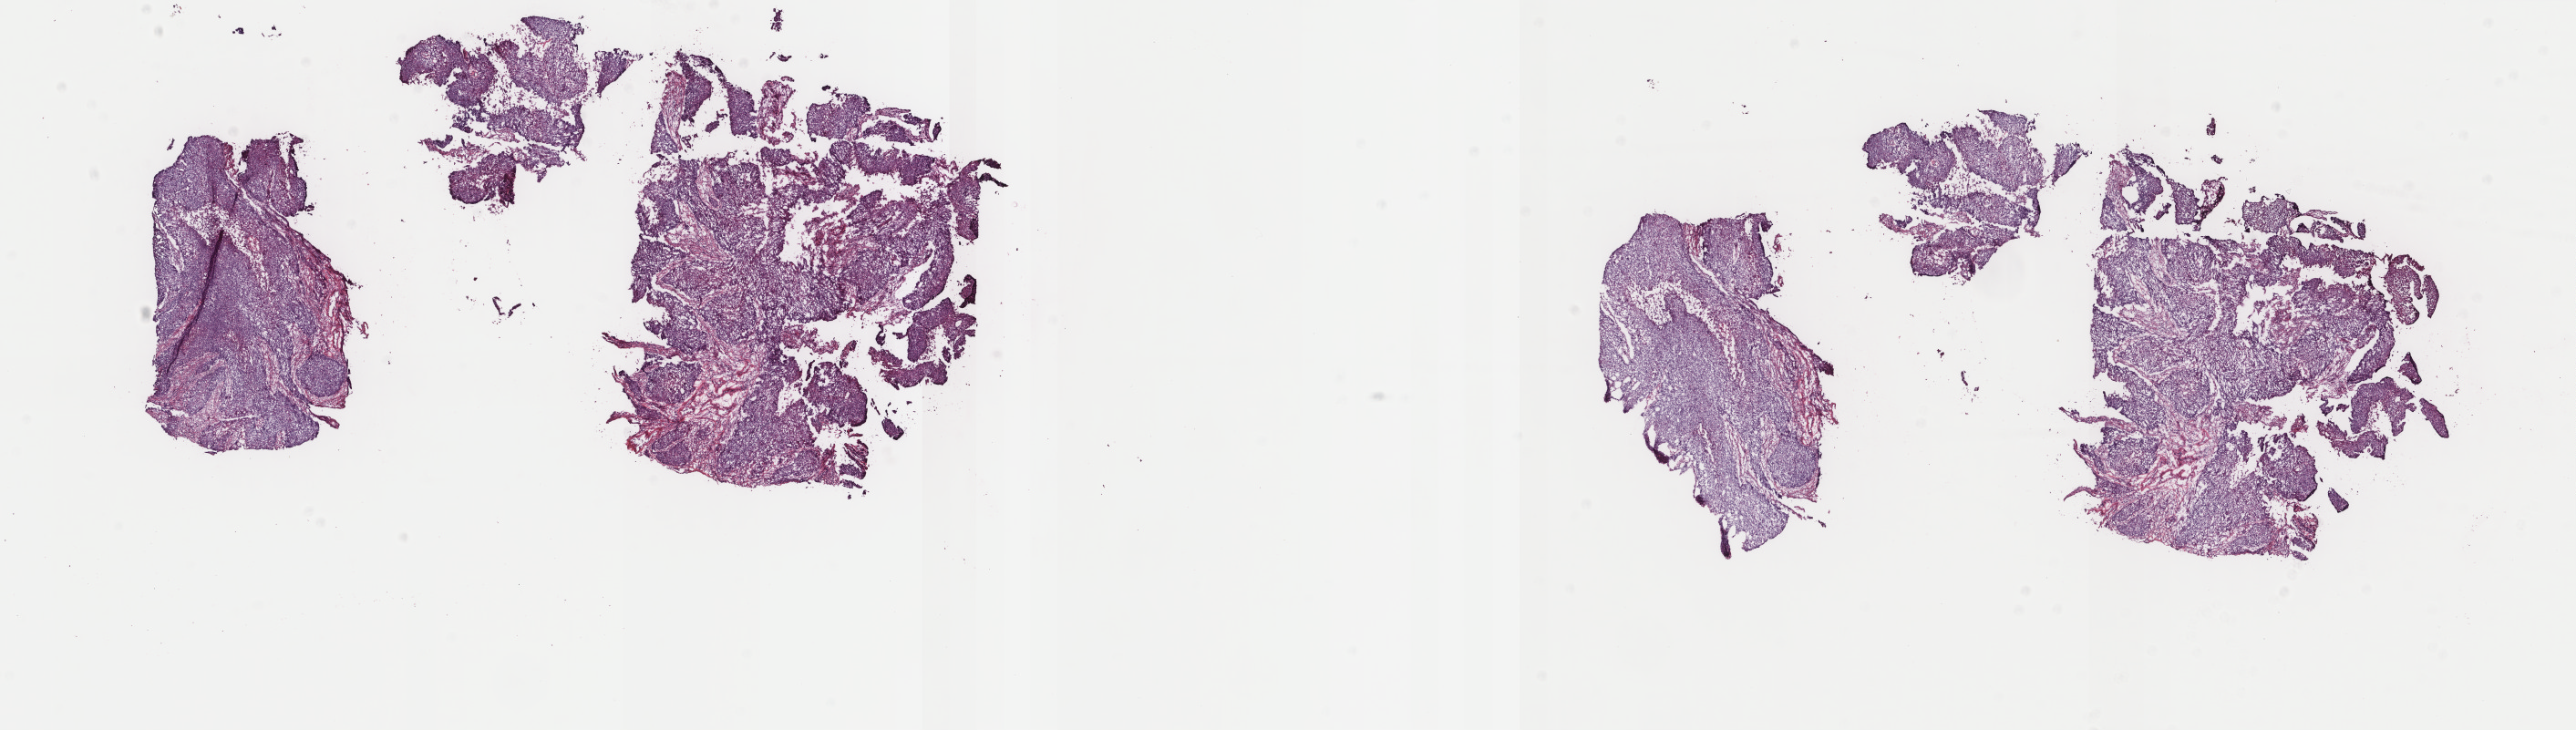
H&E whole-slide image, shown as a low-resolution overview of the whole scanned area (about 22.4 x 6.4 mm, acquisition: 40x scan); frozen section; uterus, primary tumour sample. Female patient; age at initial diagnosis 63 years. Histologic grade: G3 (poorly differentiated). Pathologist review of this section (percent, as recorded): tumour cells 83%, tumour nuclei 90%, normal cells 10%, stromal cells 5%, necrosis 2%. Inflammatory infiltration, as recorded: lymphocyte infiltration 1%, monocyte infiltration 0%, neutrophil infiltration 0%.
Lymph nodes positive (case pathology): 1 of 4 examined. FIGO stage: IIIC. Diagnosis: Endometrioid adenocarcinoma, NOS (endometrium).